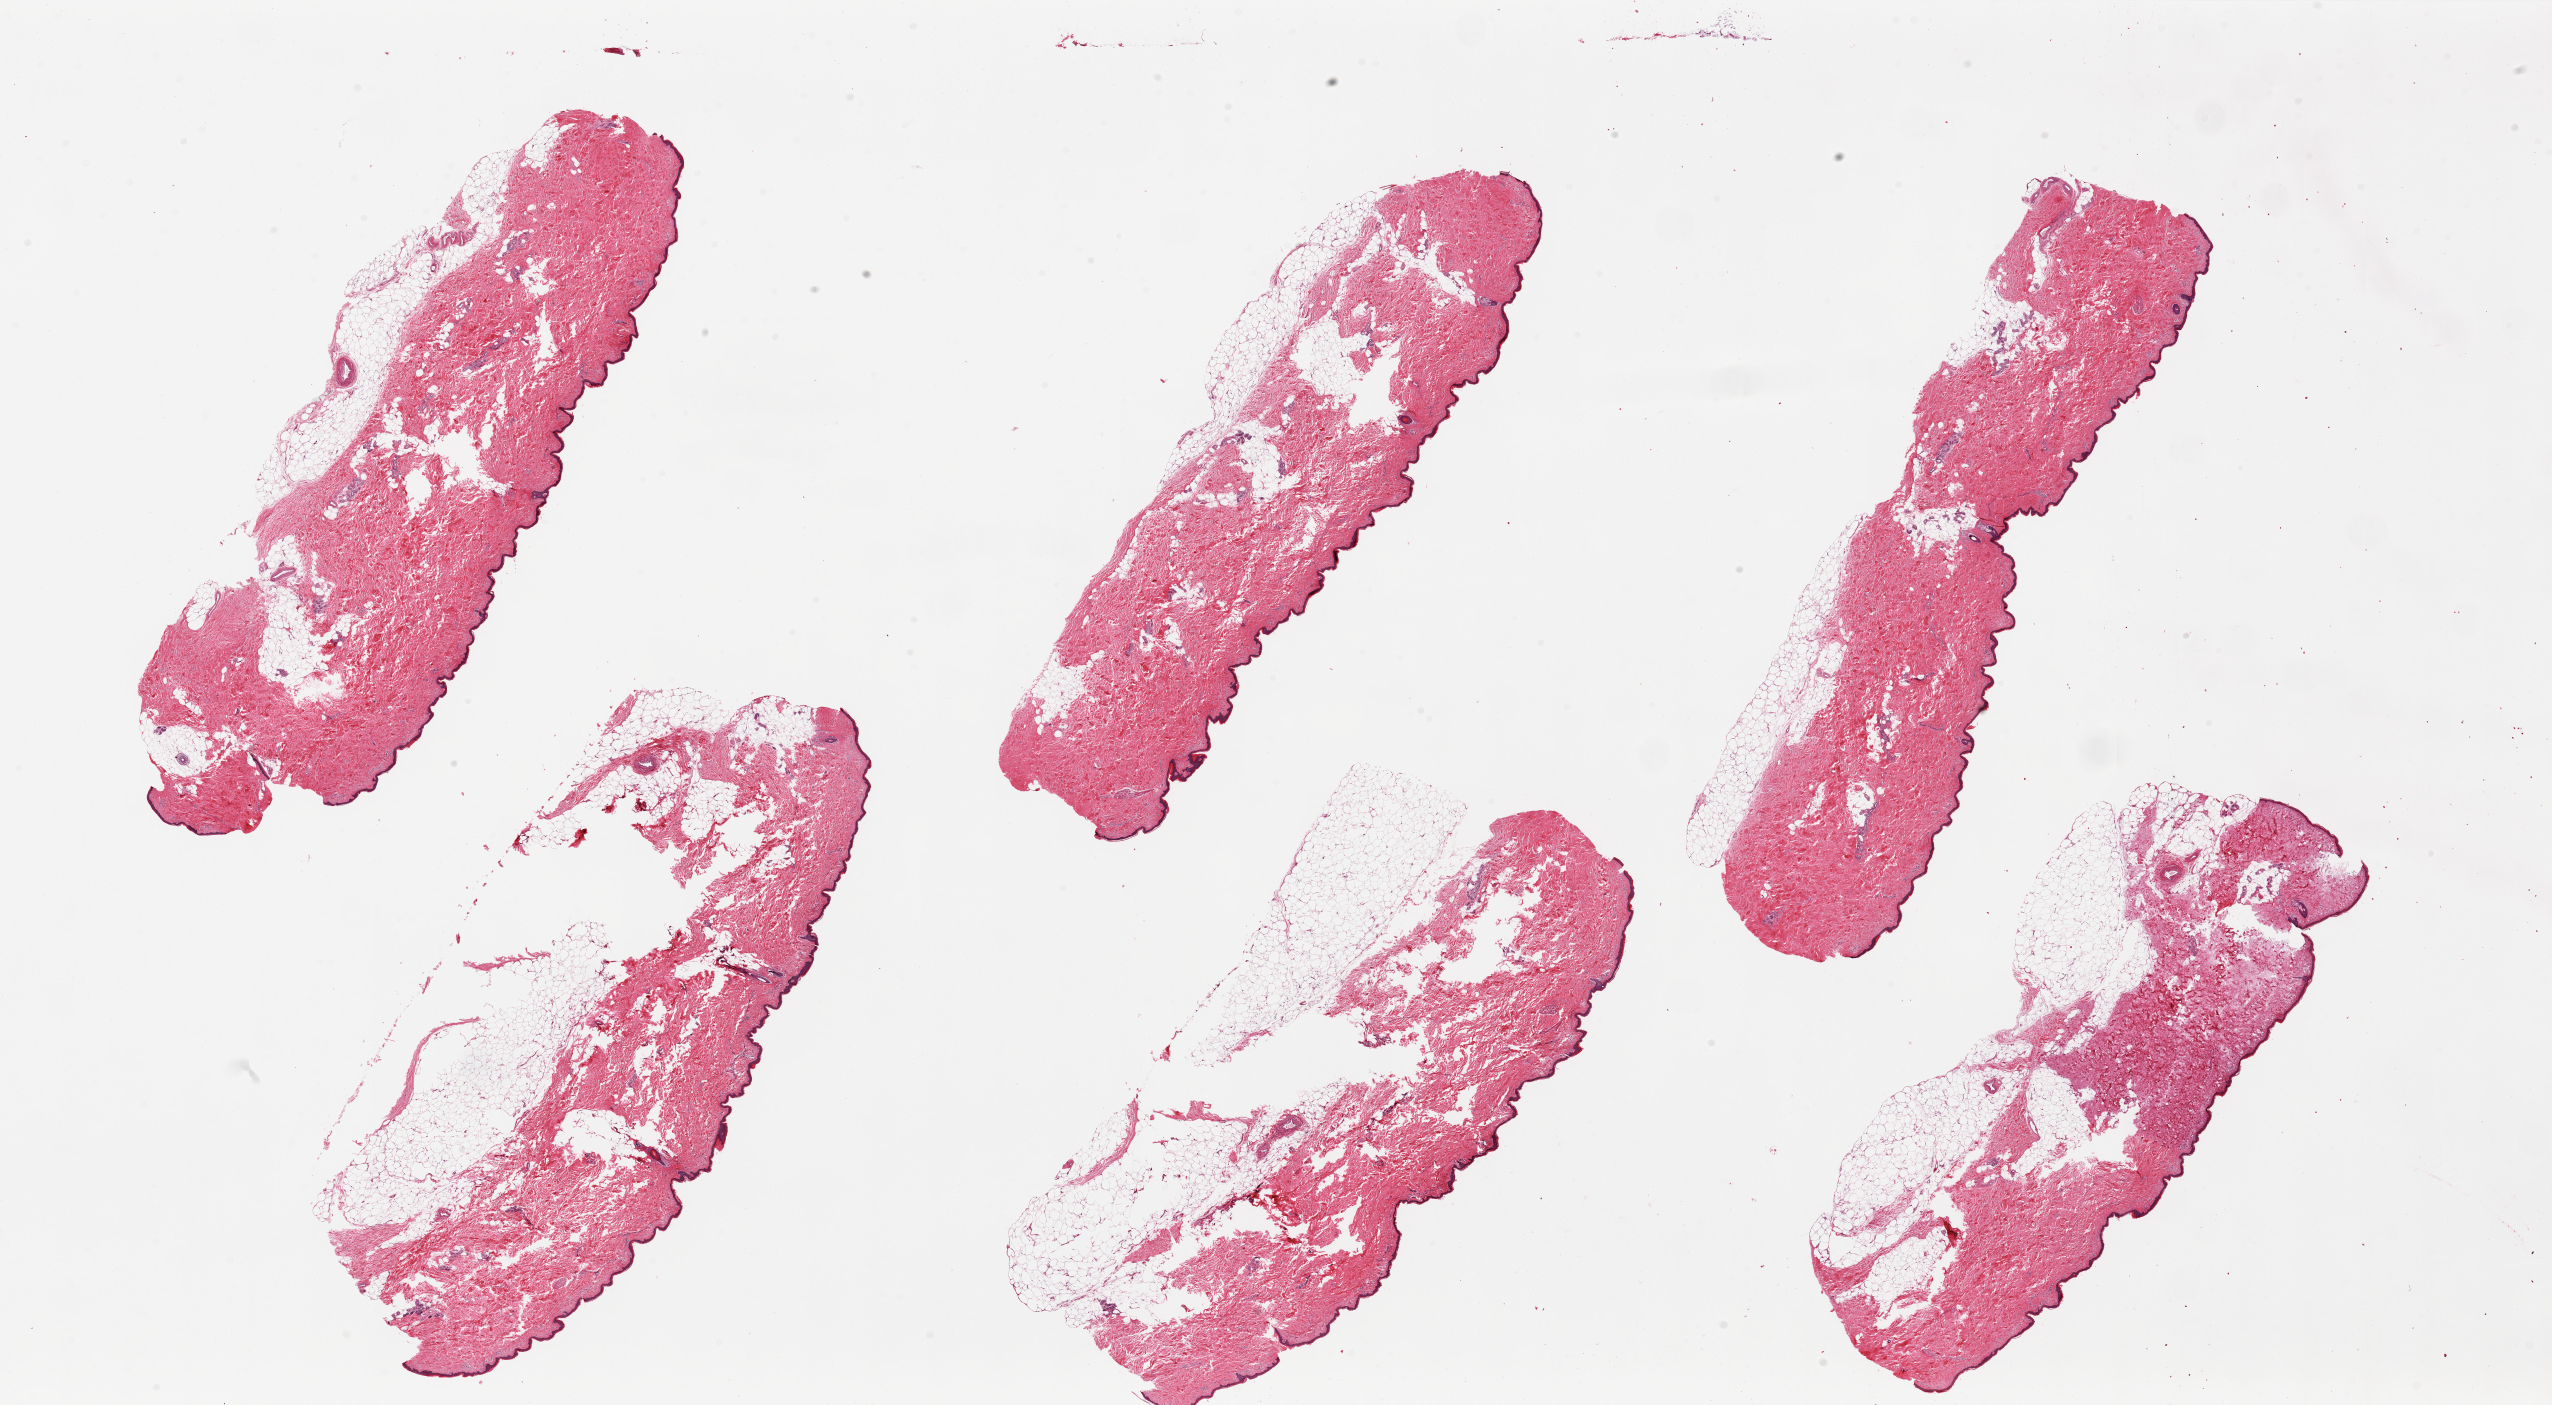
Whole-slide image, hematoxylin and eosin (H&E) stain — a low-resolution overview of the entire scanned area, about 40.4 x 22.2 mm, PAXgene-fixed, paraffin-embedded tissue, sampled site (target tissue): skin of lower leg, donor tissue sample. Female donor.
- pathologist's review note for this sample: 6 pieces , ~13x4mm : all have residual subcutaneous adipose tissue up to 2mm in thickness; skin is up to 3.5mm thick